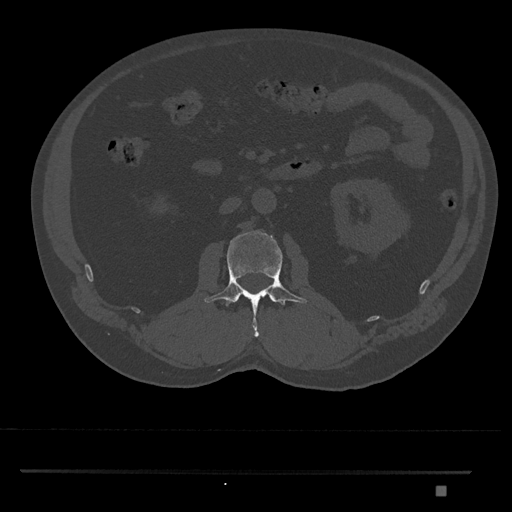
CT including the spine, one axial slice; position 754 of 1134 along the scan axis; reconstruction kernel Br40s/3; 120 kVp; bone window (W 1800 / L 400 HU); 512 × 512 image matrix, field of view 429 × 429 mm. Patient: male, 65 years. From the clinical record (not read from this slice): primary cancer: prostate.
Annotated regions visible in this slice (semi-automatically segmented with operator editing):
- L2 vertebra: box from (x=204, y=230) to (x=307, y=337) px